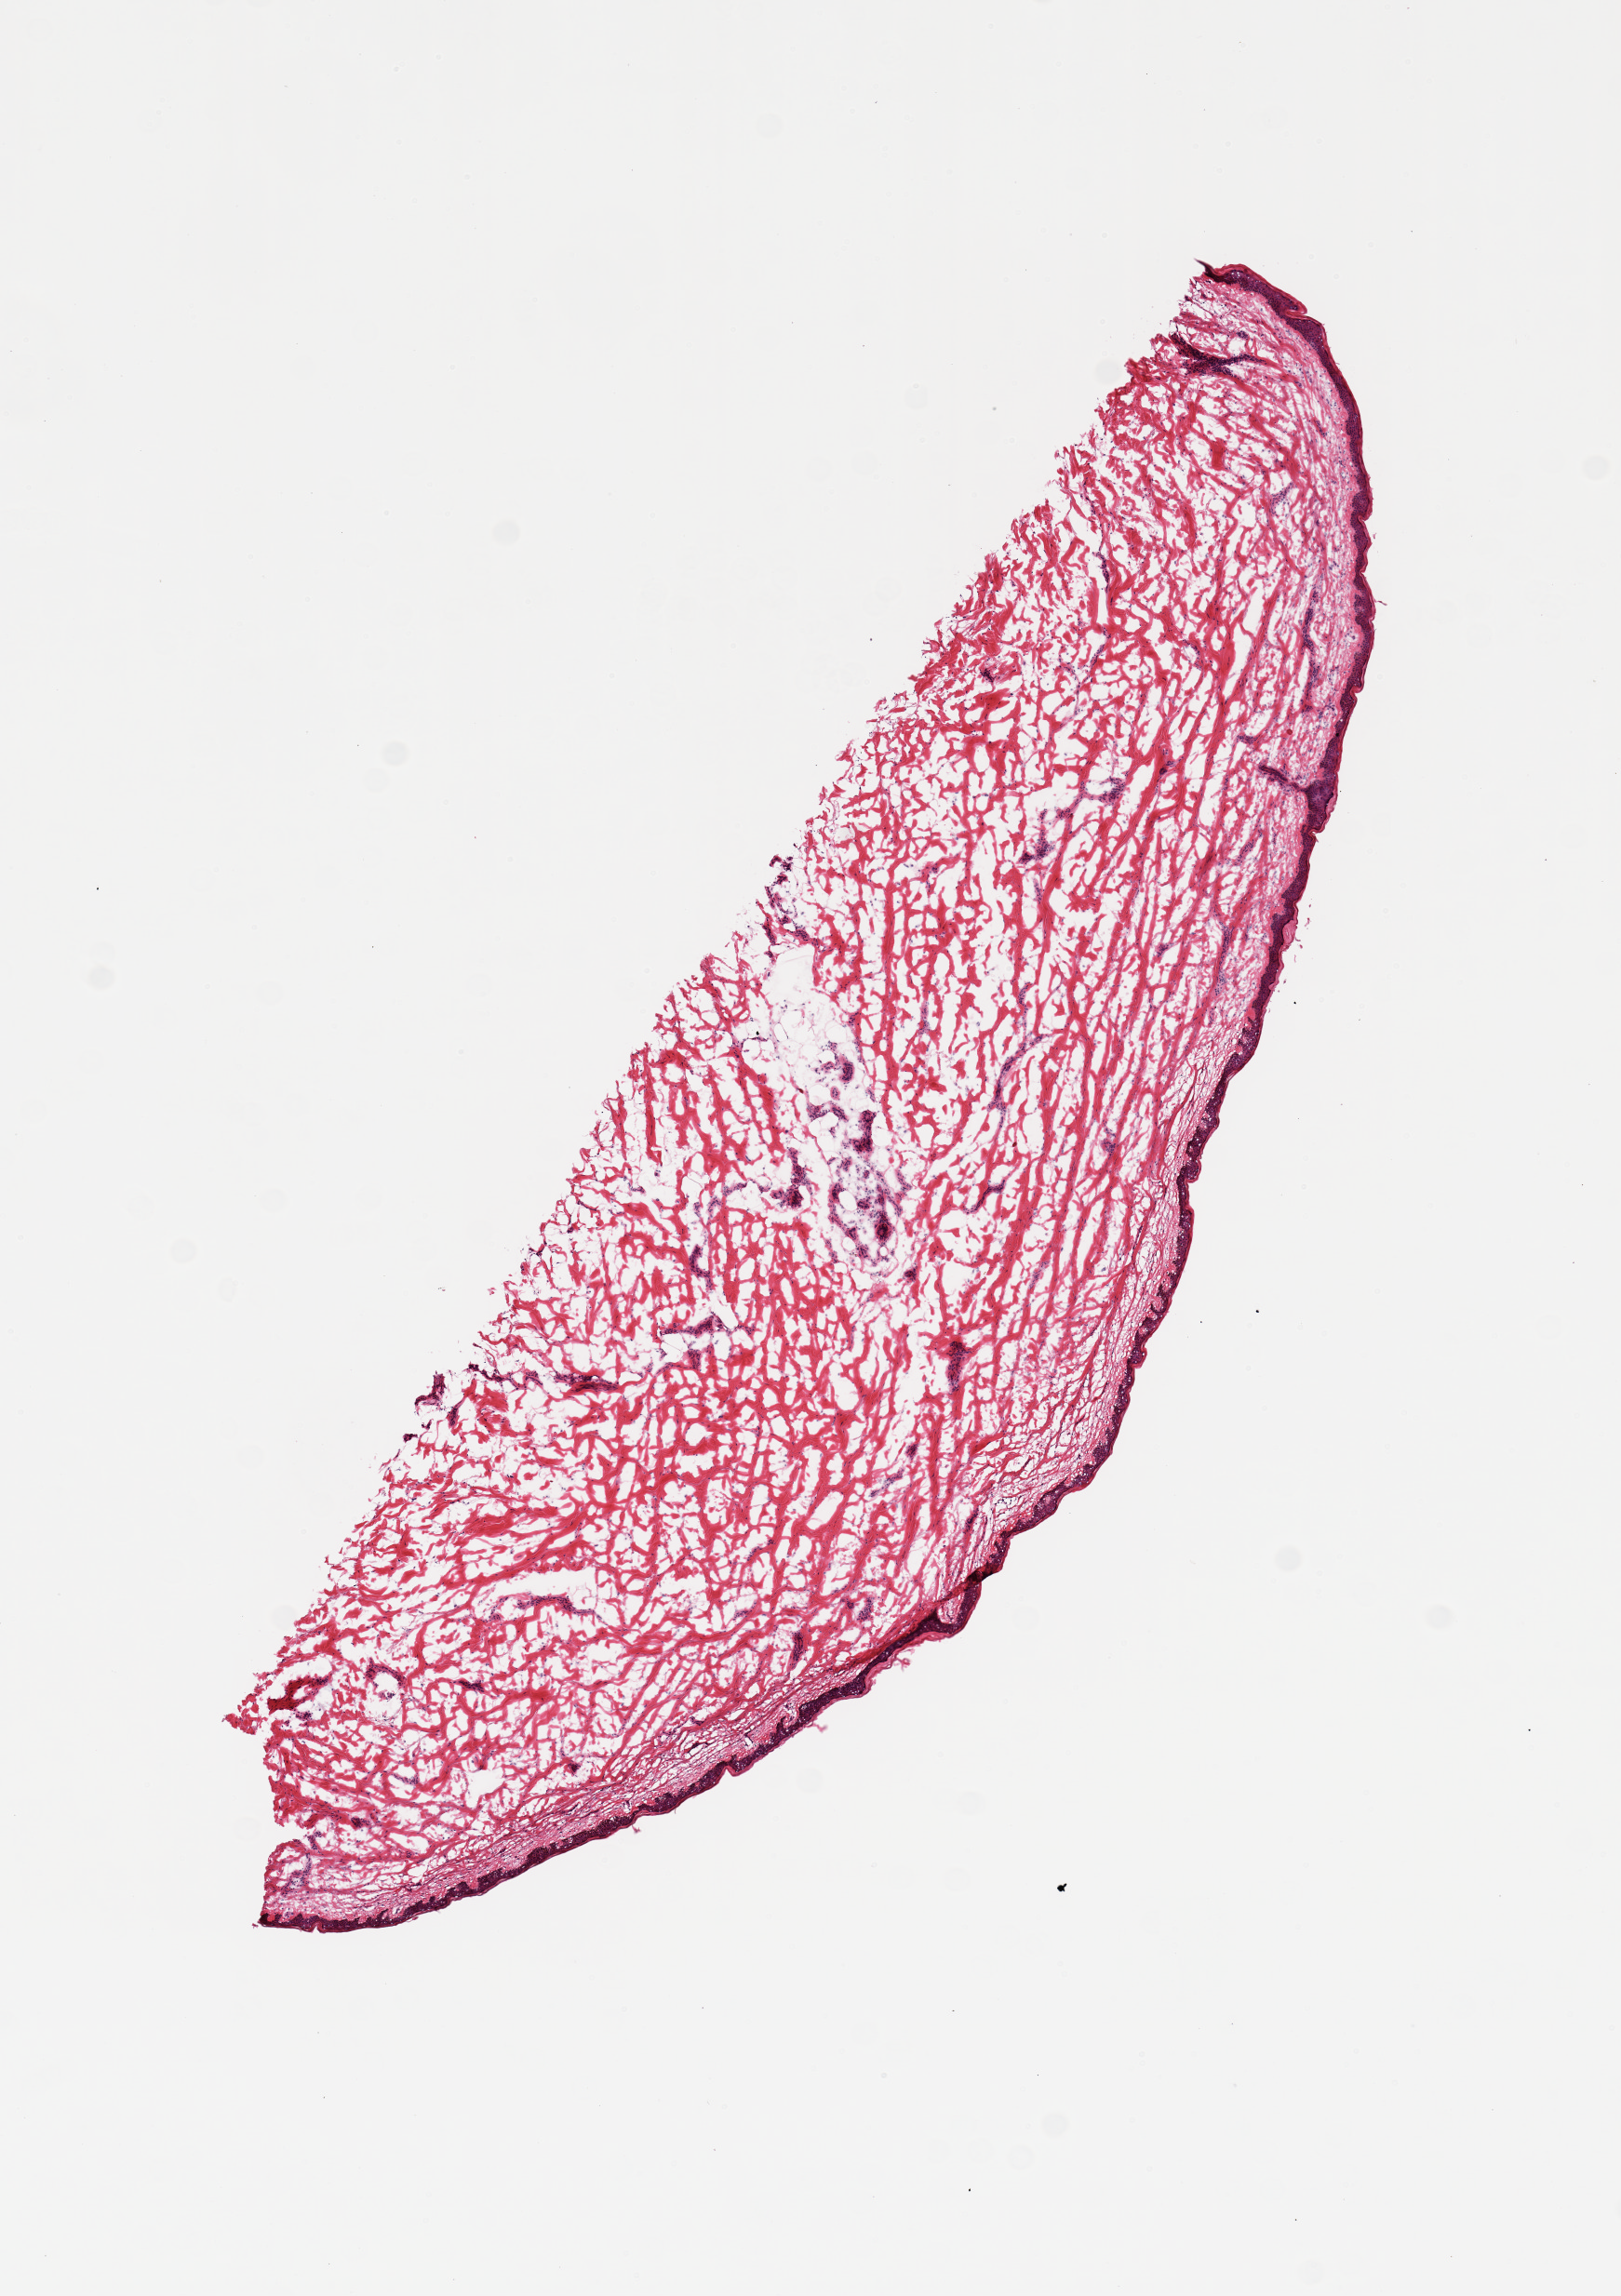
Digitized haematoxylin and eosin-stained section — shown as a low-resolution overview of the whole scanned area (about 6.9 x 9.8 mm); frozen section; section of skin of lower leg (target tissue); tissue donor sample.
* pathologist's review note for this sample: 1 piece